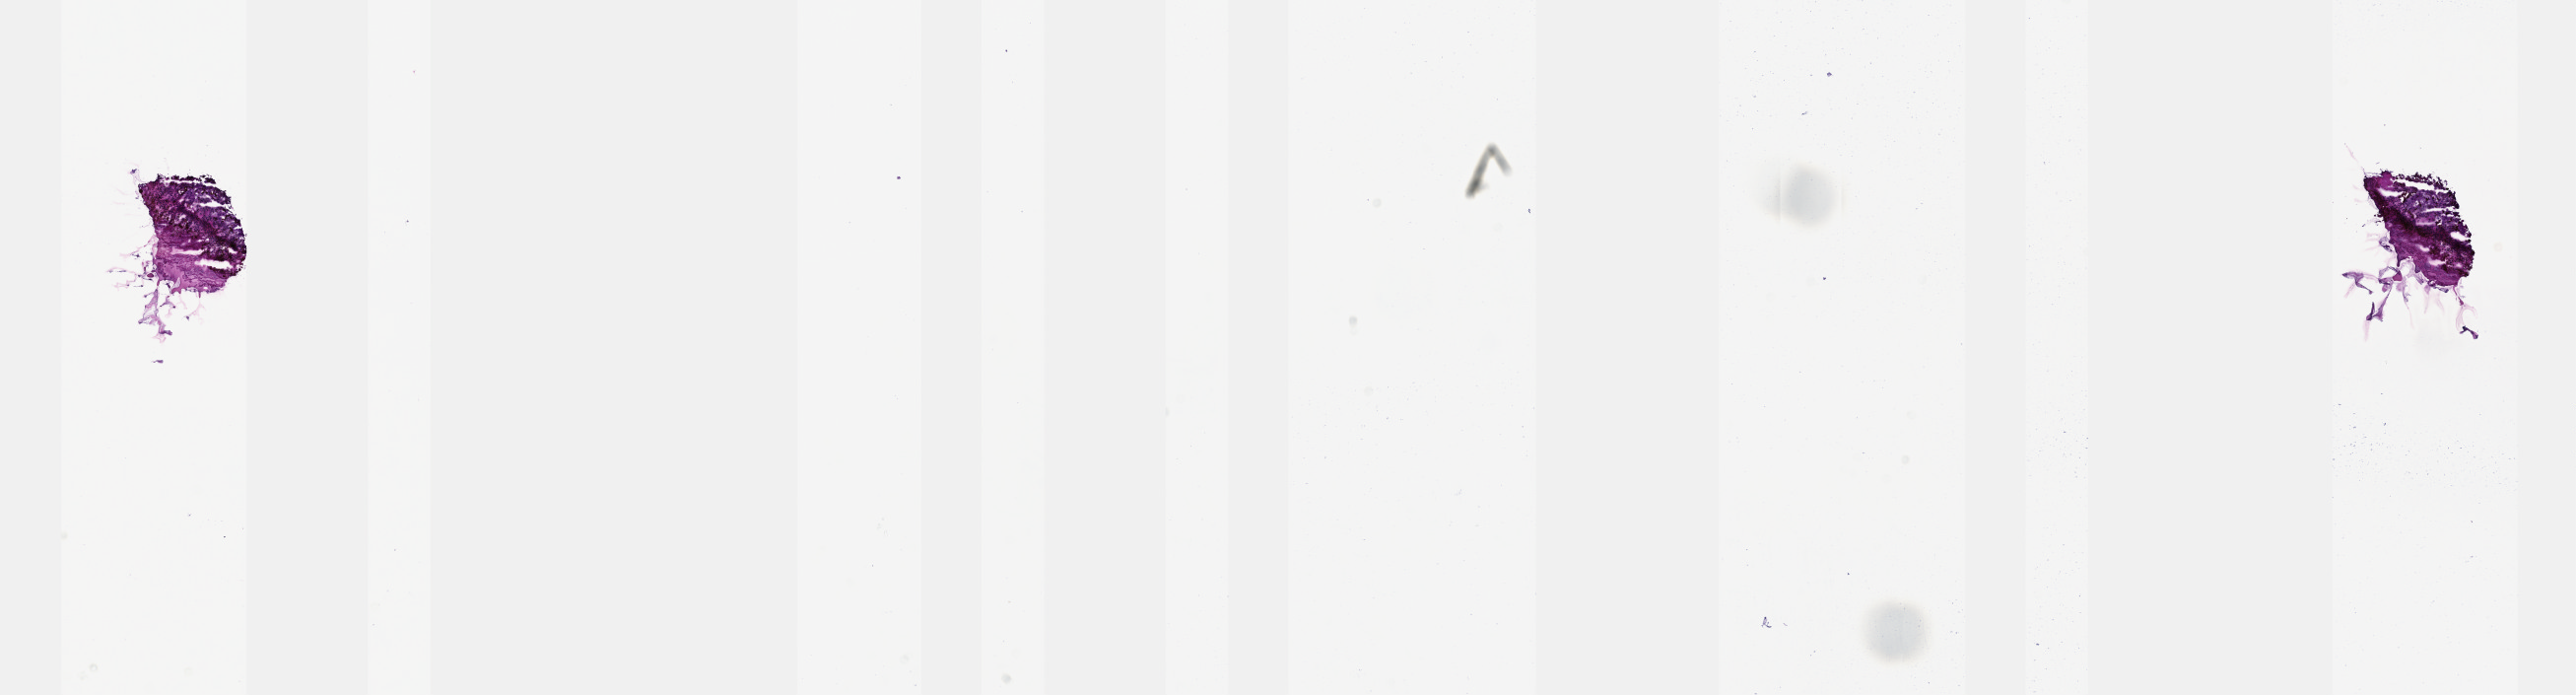
H&E-stained whole-slide image — low-resolution overview of the scanned area, about 21.1 x 5.7 mm, frozen section, uvea, primary tumour sample. Female patient; age at initial diagnosis 76 years. Slide review estimates, as recorded: tumour cells 100%, tumour nuclei 95%, normal cells 0%, stromal cells 0%, necrosis 0%. Infiltration values recorded for this section: lymphocyte infiltration 0%, monocyte infiltration 0%, neutrophil infiltration 0%.
• histologic diagnosis: Mixed epithelioid and spindle cell melanoma
• AJCC pathologic stage: IIIA (7th edition)